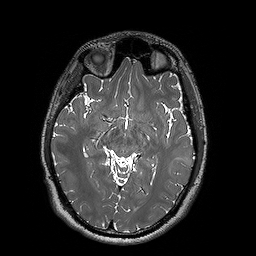
Brain MRI from a brain-tumour surgery series, one axial slice. Position 97 of 192 along the scan axis. 256 × 256 image matrix. From the clinical record (not read from this slice): histopathology: Oligodendroglioma; WHO grade: 2.
Structures marked on this image (manually delineated by an expert):
- tumour: box from (x=163, y=155) to (x=186, y=172) px